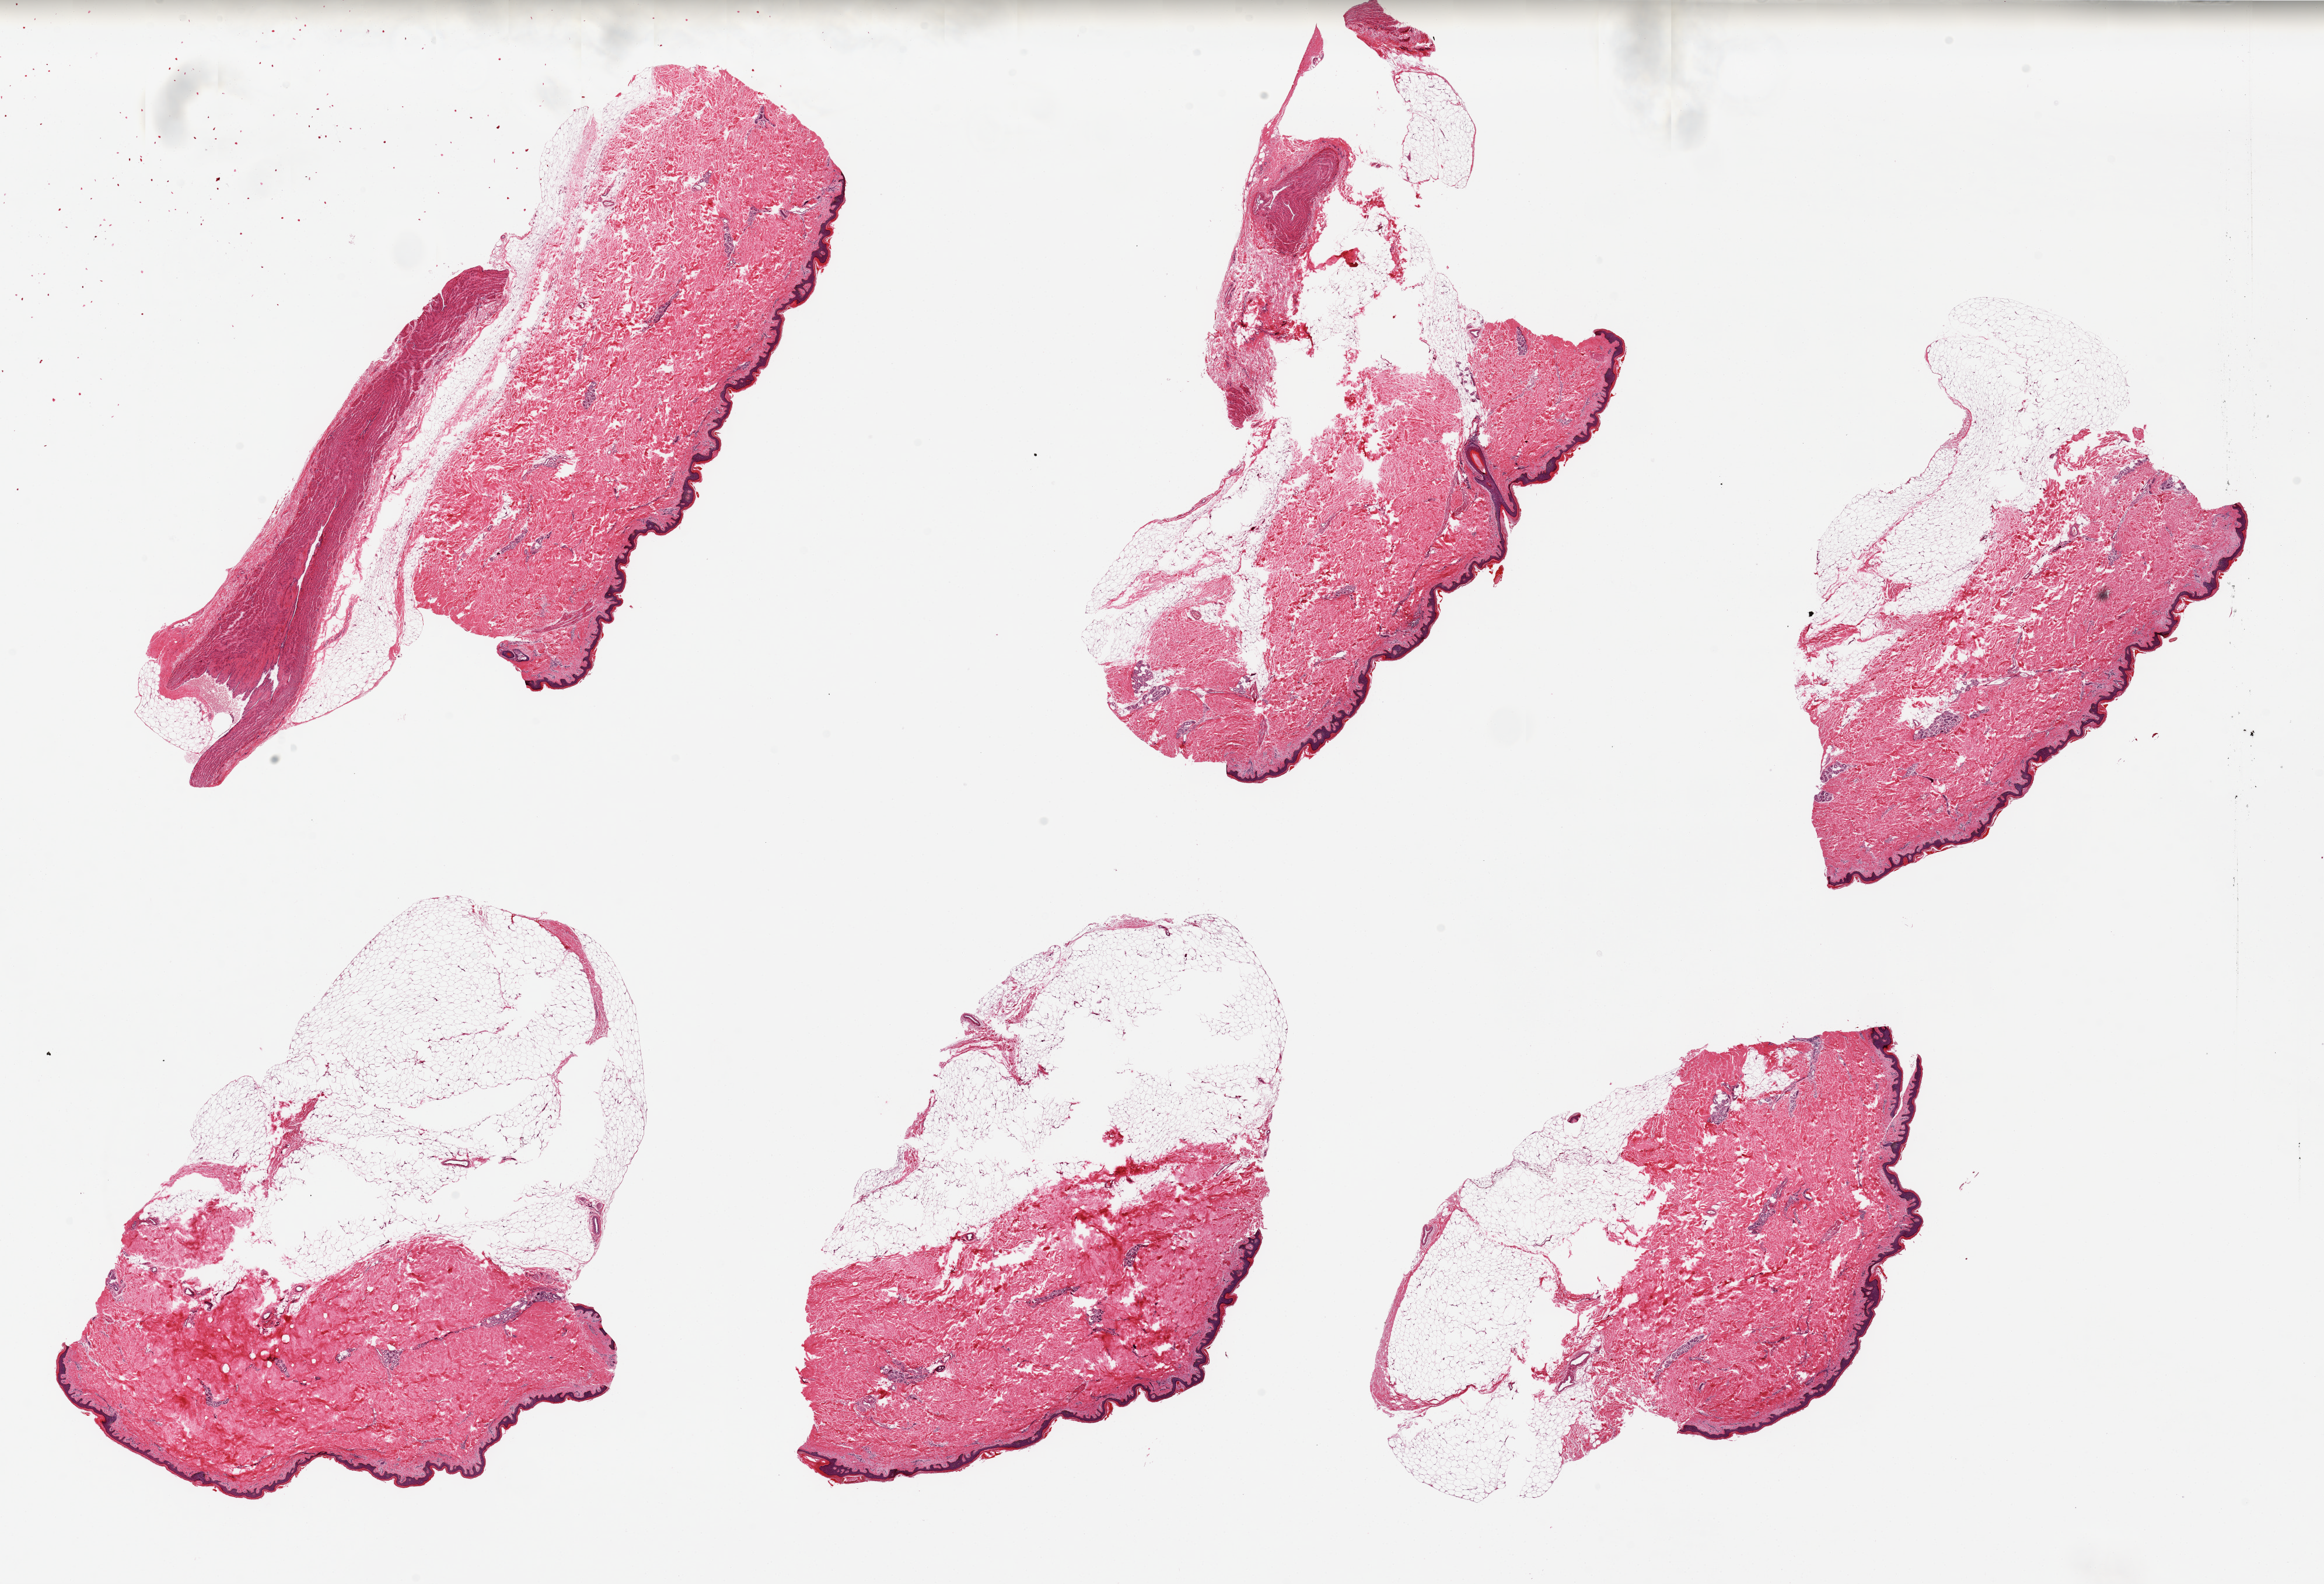
Digitized hematoxylin and eosin (H&E)-stained section — a low-resolution overview of the entire scanned area, about 31.5 x 21.5 mm, PAXgene-fixed, paraffin-embedded tissue, section of skin of lower leg (target tissue), donor tissue sample. Donor sex: male.
Review note (as recorded): 6 pieces, up to 12x5.5mm. All have large amounts of subcutaneous adipose tissue, up to 4.7 mm thick (skin is 3mm thick); 2 have attached subcutaneous veins.